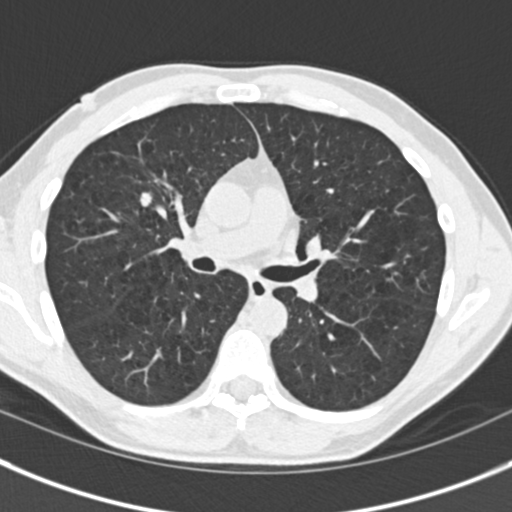
Low-dose screening chest CT, one axial slice; slice 99 of 175 in the series (ordered by position); reconstruction kernel B30f; 120 kVp; lung window (W 1500 / L -600 HU); 2 mm slice thickness; 512 × 512 image matrix, field of view 306 × 306 mm.
Outlined on this slice (outlined manually by an expert reader):
- lesion 1 (tumor, upper lobe of right lung): bounding box (x1, y1, x2, y2) in pixels: (140, 192, 152, 207)